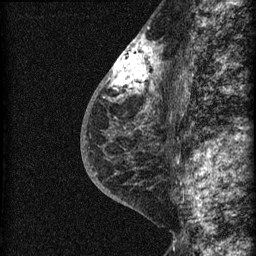
Breast MRI (dynamic contrast-enhanced), one sagittal slice; position 35 of 60 along the scan axis; dynamic contrast-enhanced series, image 2 of 3 at this slice position (ordered by acquisition); 1.5 T; TE 4.2 ms, TR 22.7 ms; 256 × 256 image matrix, field of view 180 × 180 mm. Patient: female, 48 years. From the clinical record (not read from this slice): setting: breast cancer imaged before/during neoadjuvant chemotherapy; receptor status: triple-negative.
Outlined on this slice (semi-automatic segmentation, software-assisted and operator-edited):
- analysis volume of interest (the breast-tissue region the enhancement analysis was run in; not a lesion): bounding box [x1, y1, x2, y2] px = [115, 34, 169, 162]
- tumour enhancement mask (voxels above the 90 % enhancement threshold inside the analysis volume of interest): [115, 35, 158, 93]